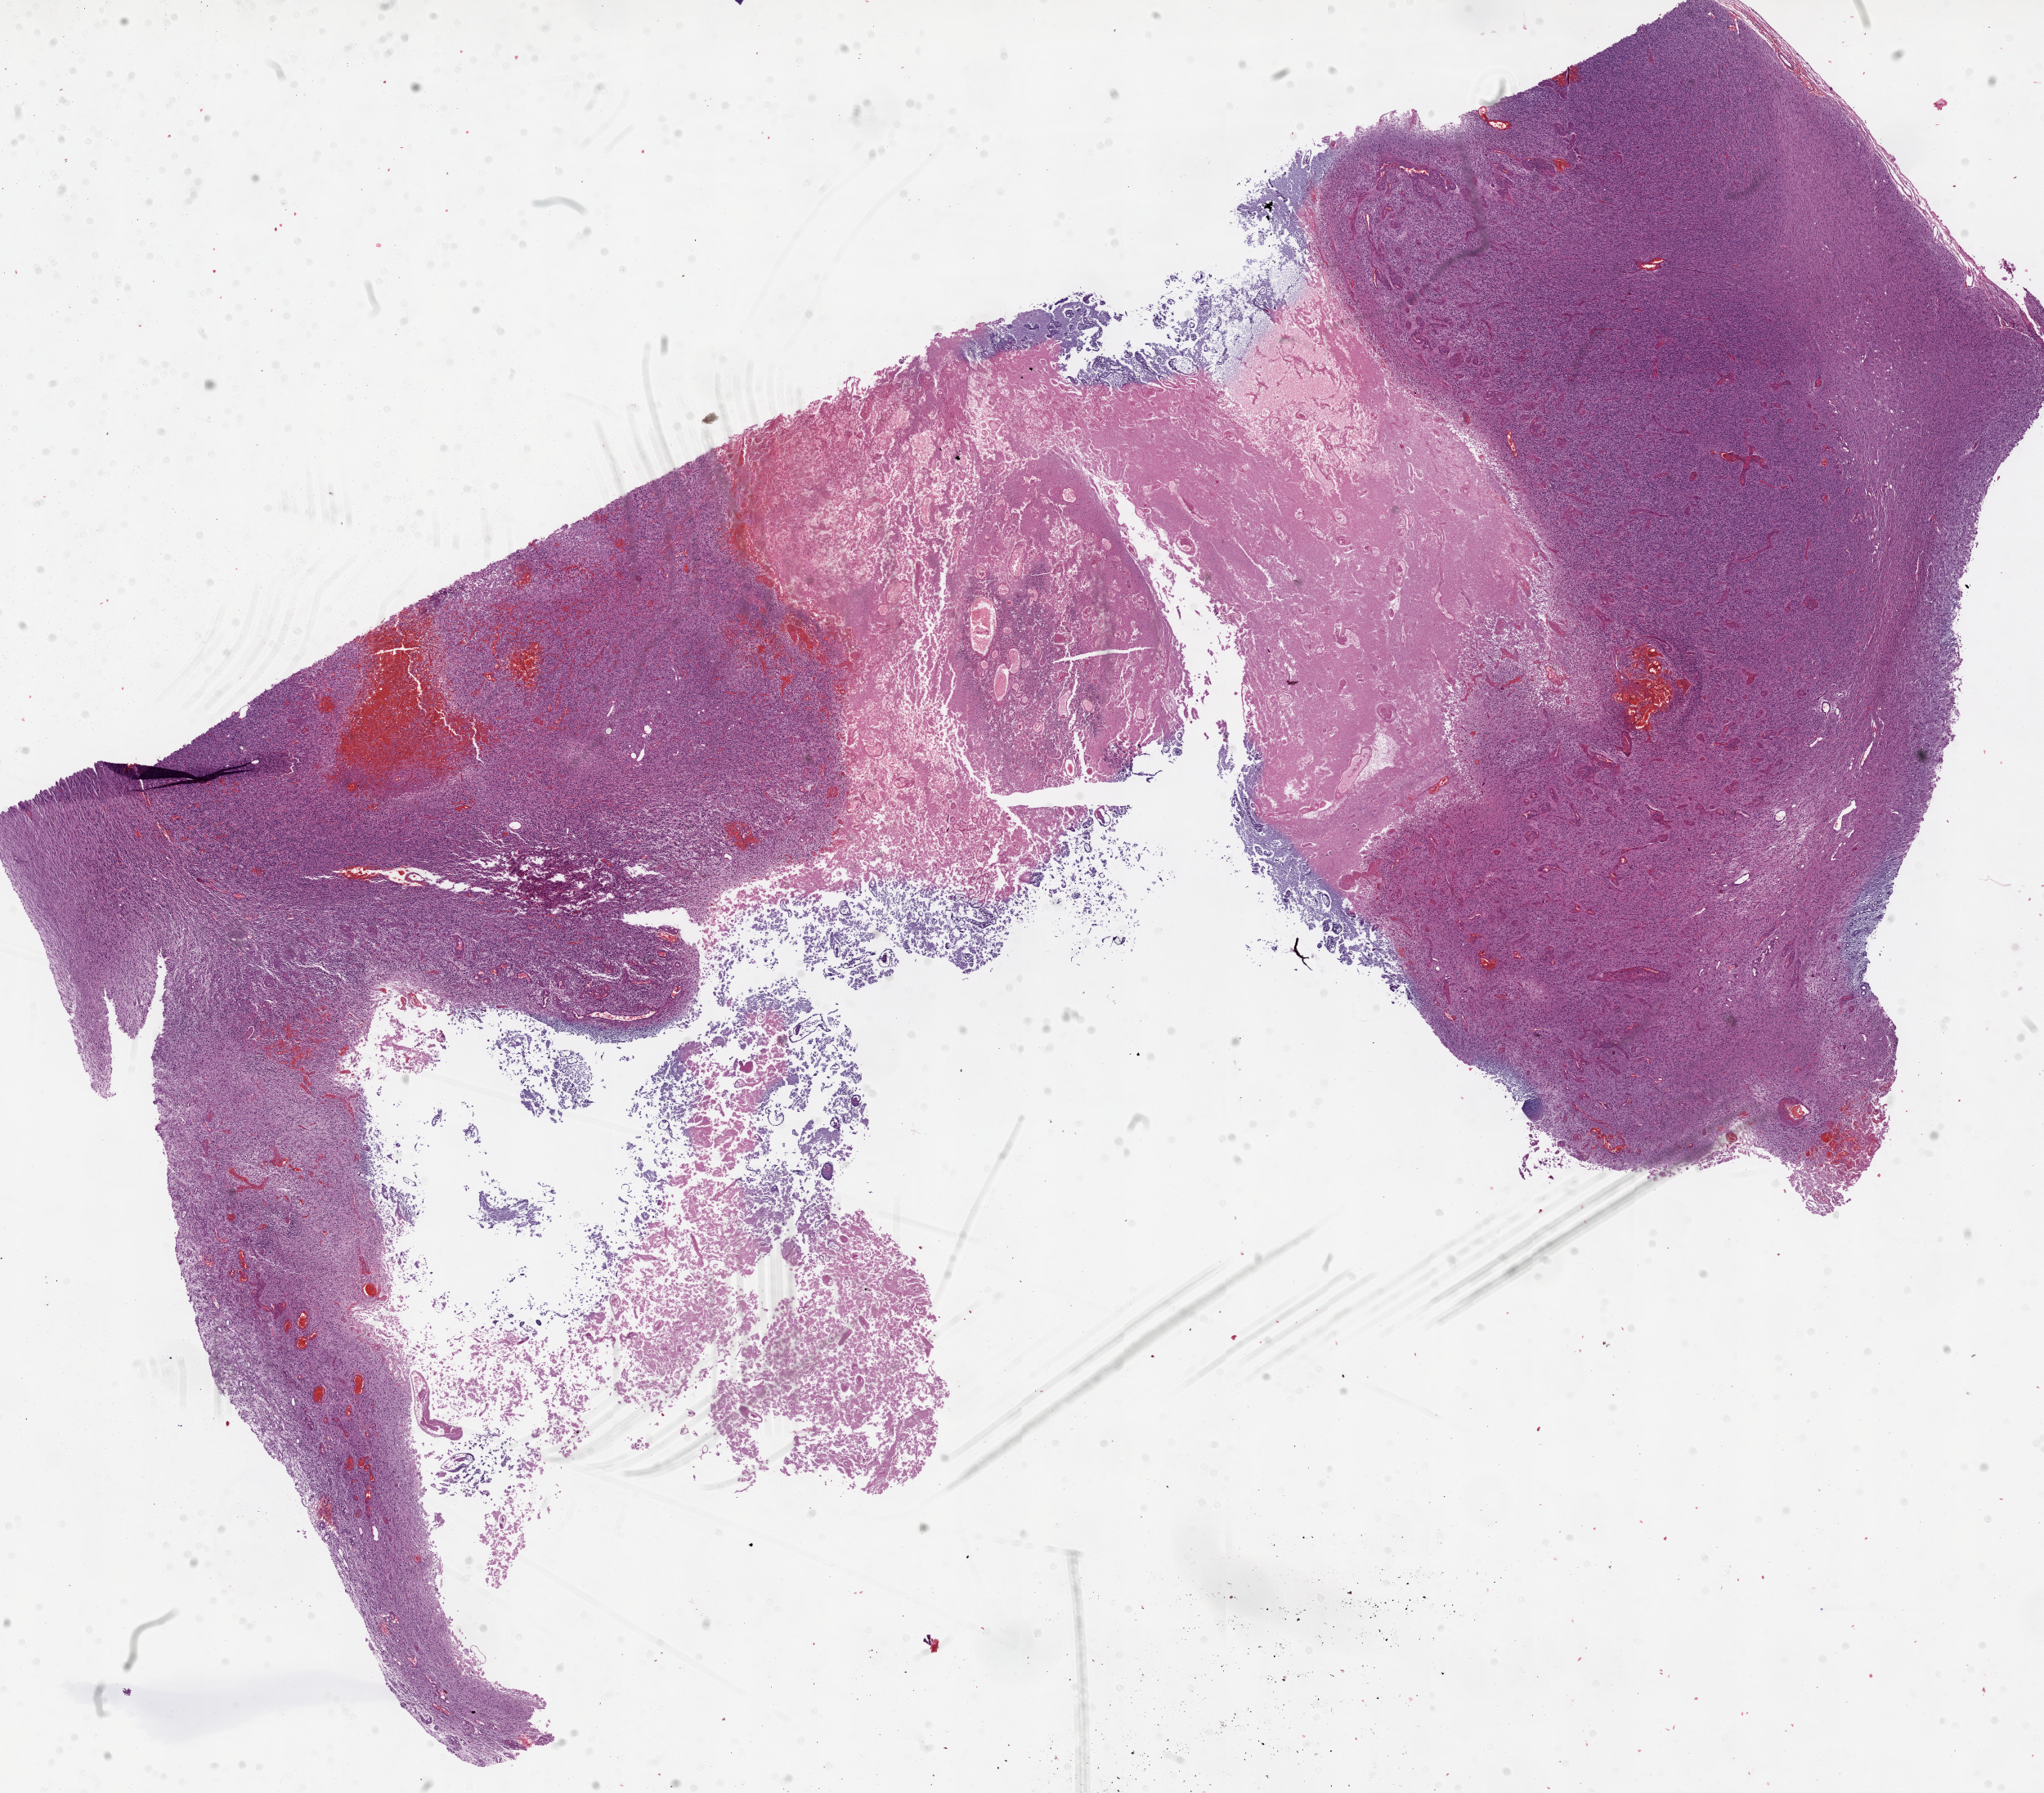
Whole-slide histology image, H&E — whole scanned area (about 20.1 x 17.6 mm, slide scanned at 20x) shown as a low-resolution overview; formalin-fixed paraffin-embedded (FFPE) diagnostic section; sample: primary tumour, brain. Patient: male, age at initial diagnosis 68 years.
Diagnosis: Glioblastoma.